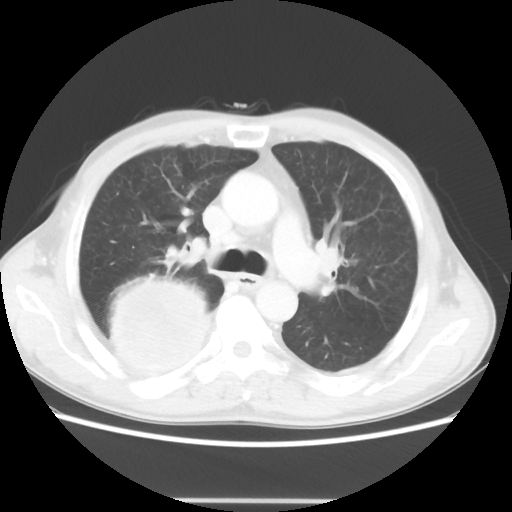
Chest CT, one axial slice; position 32 of 48 along the scan axis; reconstruction kernel STANDARD; 100 kVp; lung window (W 1500 / L -600 HU); 5 mm slice thickness; 512 × 512 image matrix. Male patient, age 66 years. From the clinical record (not read from this slice): clinical TNM (as recorded): T4 N1 M1; histopathological grade: G3.
Structures marked on this image (bounding box drawn by a radiologist):
- lung tumour (recorded histology: small cell carcinoma): bounding box [x1, y1, x2, y2] px = [101, 274, 211, 377]